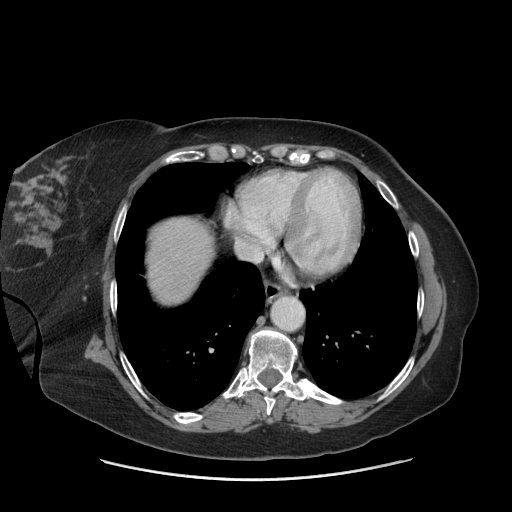
Contrast-enhanced abdominal CT (liver protocol), one axial slice; slice 68 of 69 in the series (ordered by position); 140 kVp; soft-tissue window (W 400 / L 40 HU); 512 × 512 image matrix. From the clinical record (not read from this slice): diagnosis: hepatocellular carcinoma (patient treated with transarterial chemoembolisation; whether this scan precedes or follows treatment is not stated here); TNM stage (as recorded): Stage-IIIB; Child-Pugh class: A; tumour differentiation: moderately differentiated; tumour nodularity: multinodular.
Structures marked on this image (semi-automatically segmented with operator editing):
- abdominal aorta: bounding box [x1, y1, x2, y2] px = [272, 298, 302, 330]
- liver parenchyma outside the tumour (the mass and vessels are separate outlines, so this box may not span the whole liver): [148, 218, 212, 302]